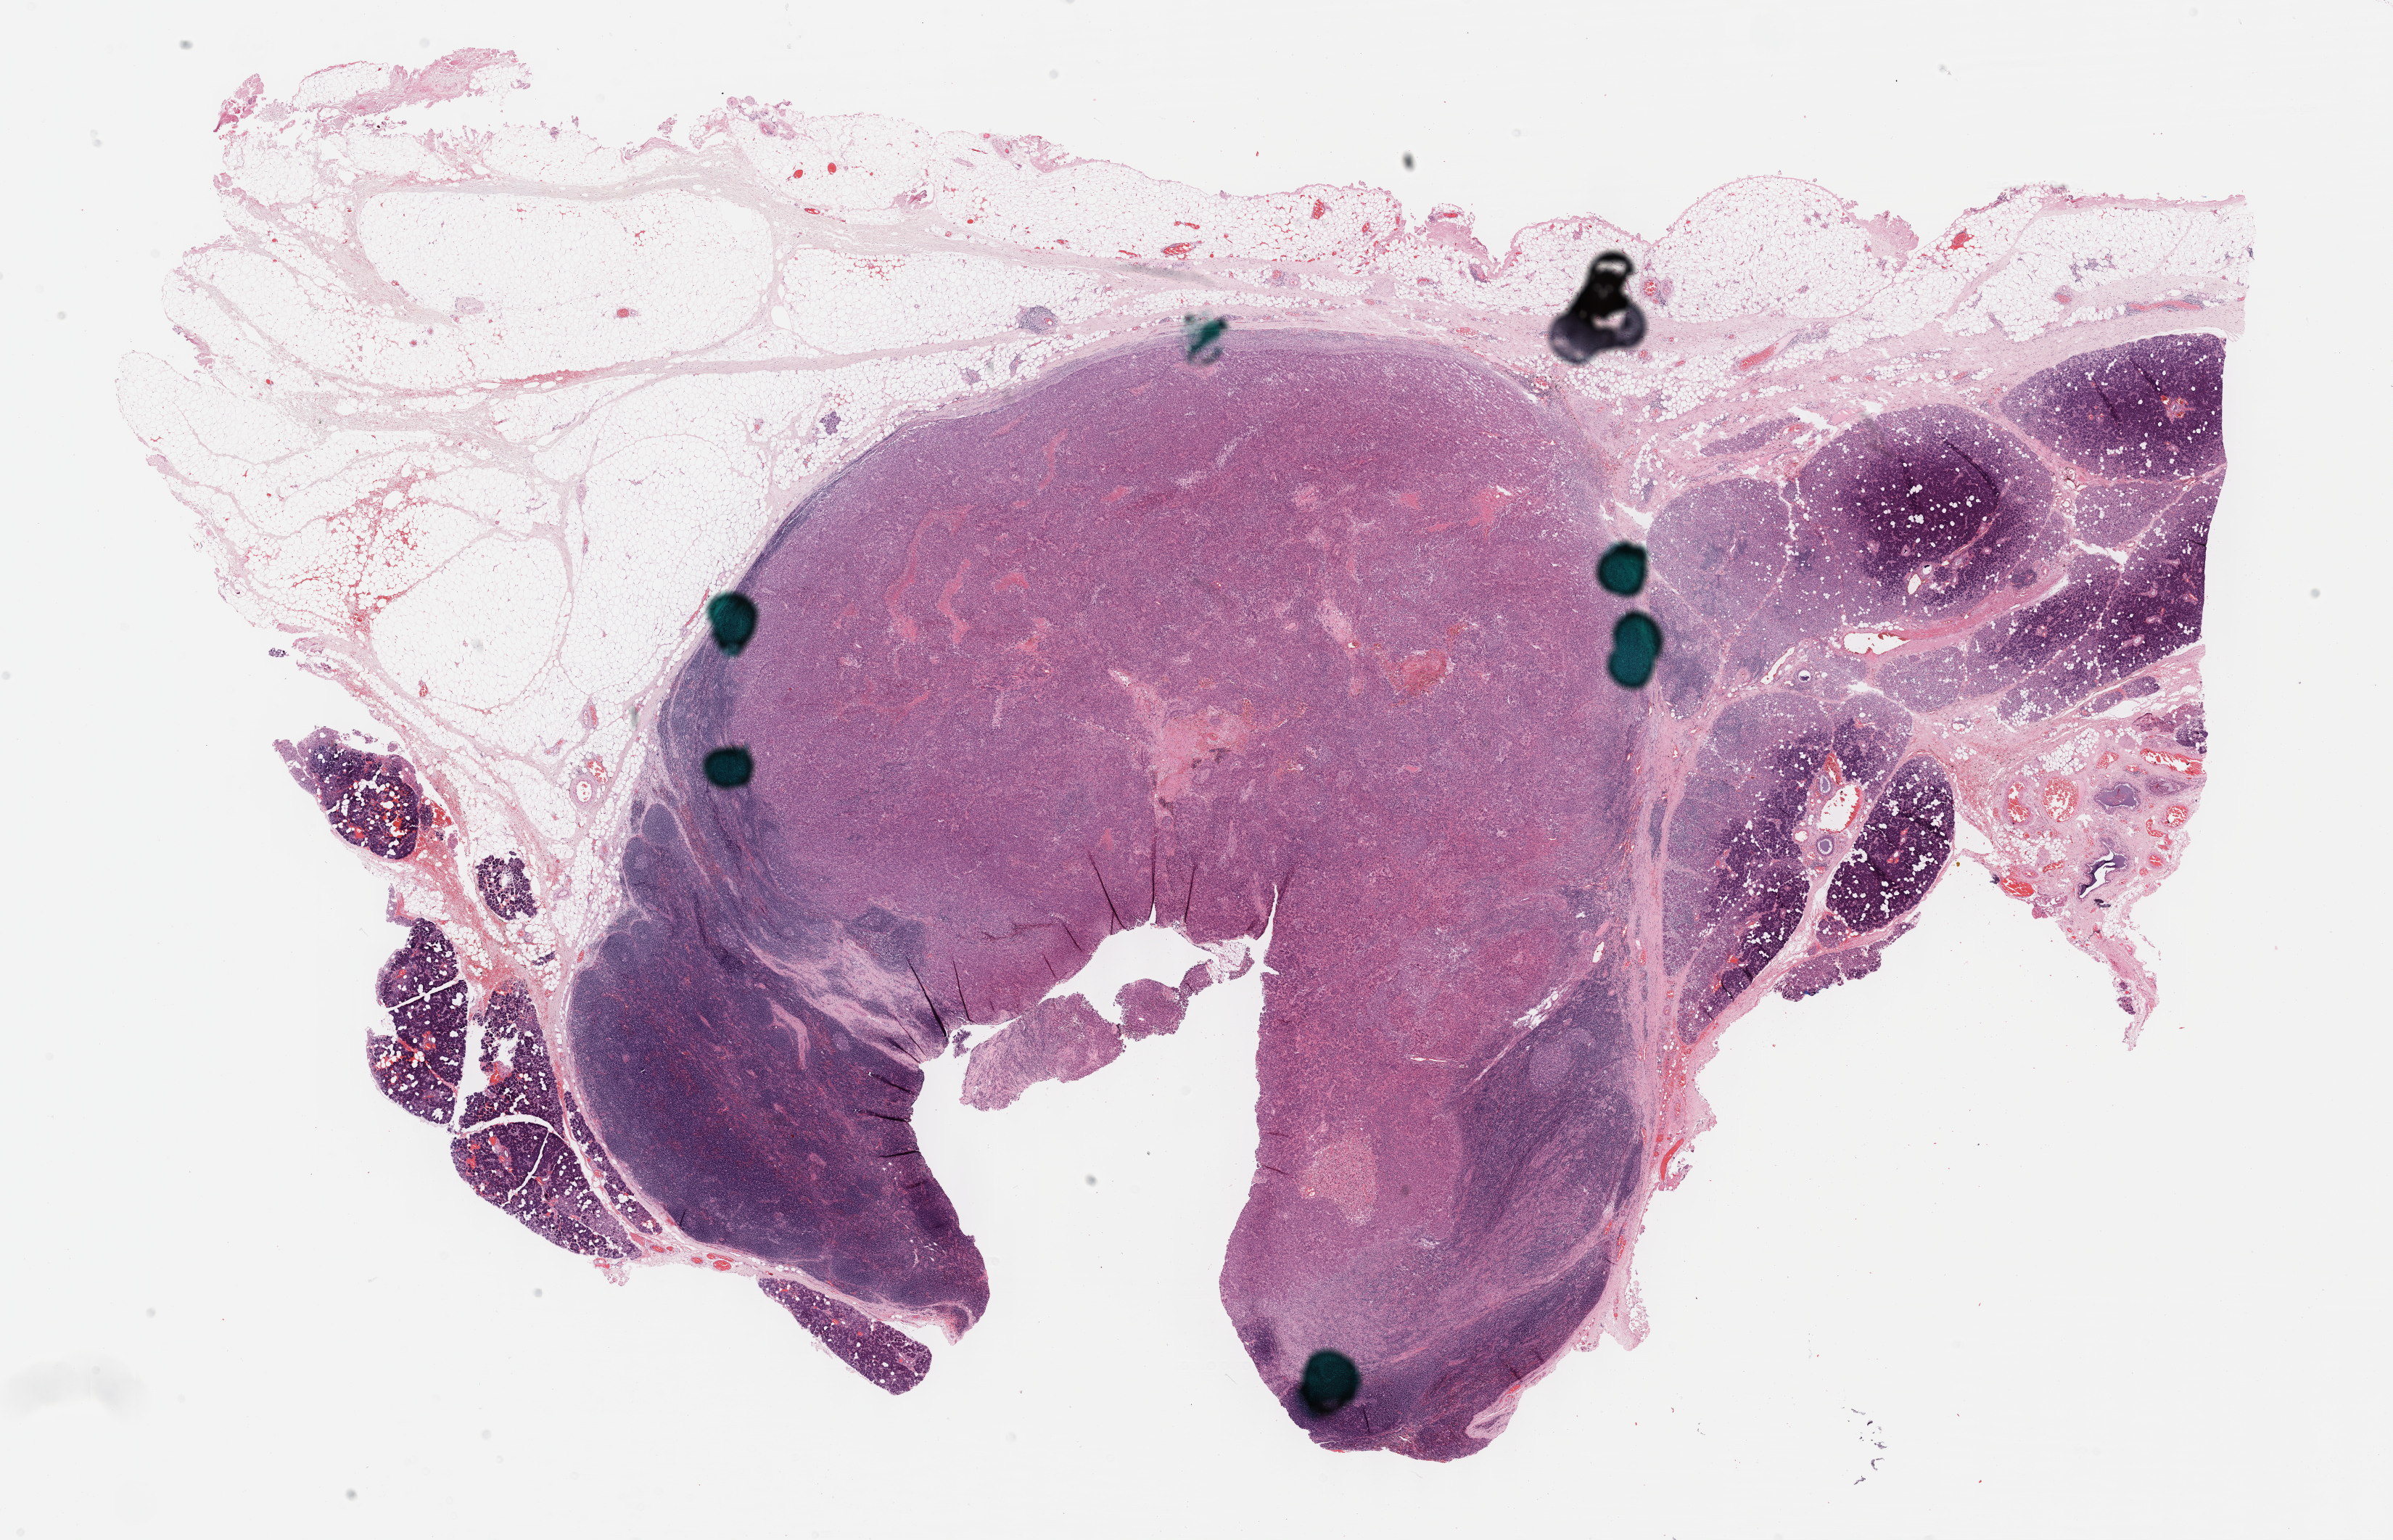
Digitized Hematoxylin and eosin (H&E) stained tissue section (whole slide), a low-resolution overview of the entire scanned area, about 26.7 x 17.2 mm; FFPE section; metastatic tumour sample. Male, age 47 years at initial diagnosis.
* this section: metastatic tumour tissue
* patient diagnosis: Malignant melanoma, NOS